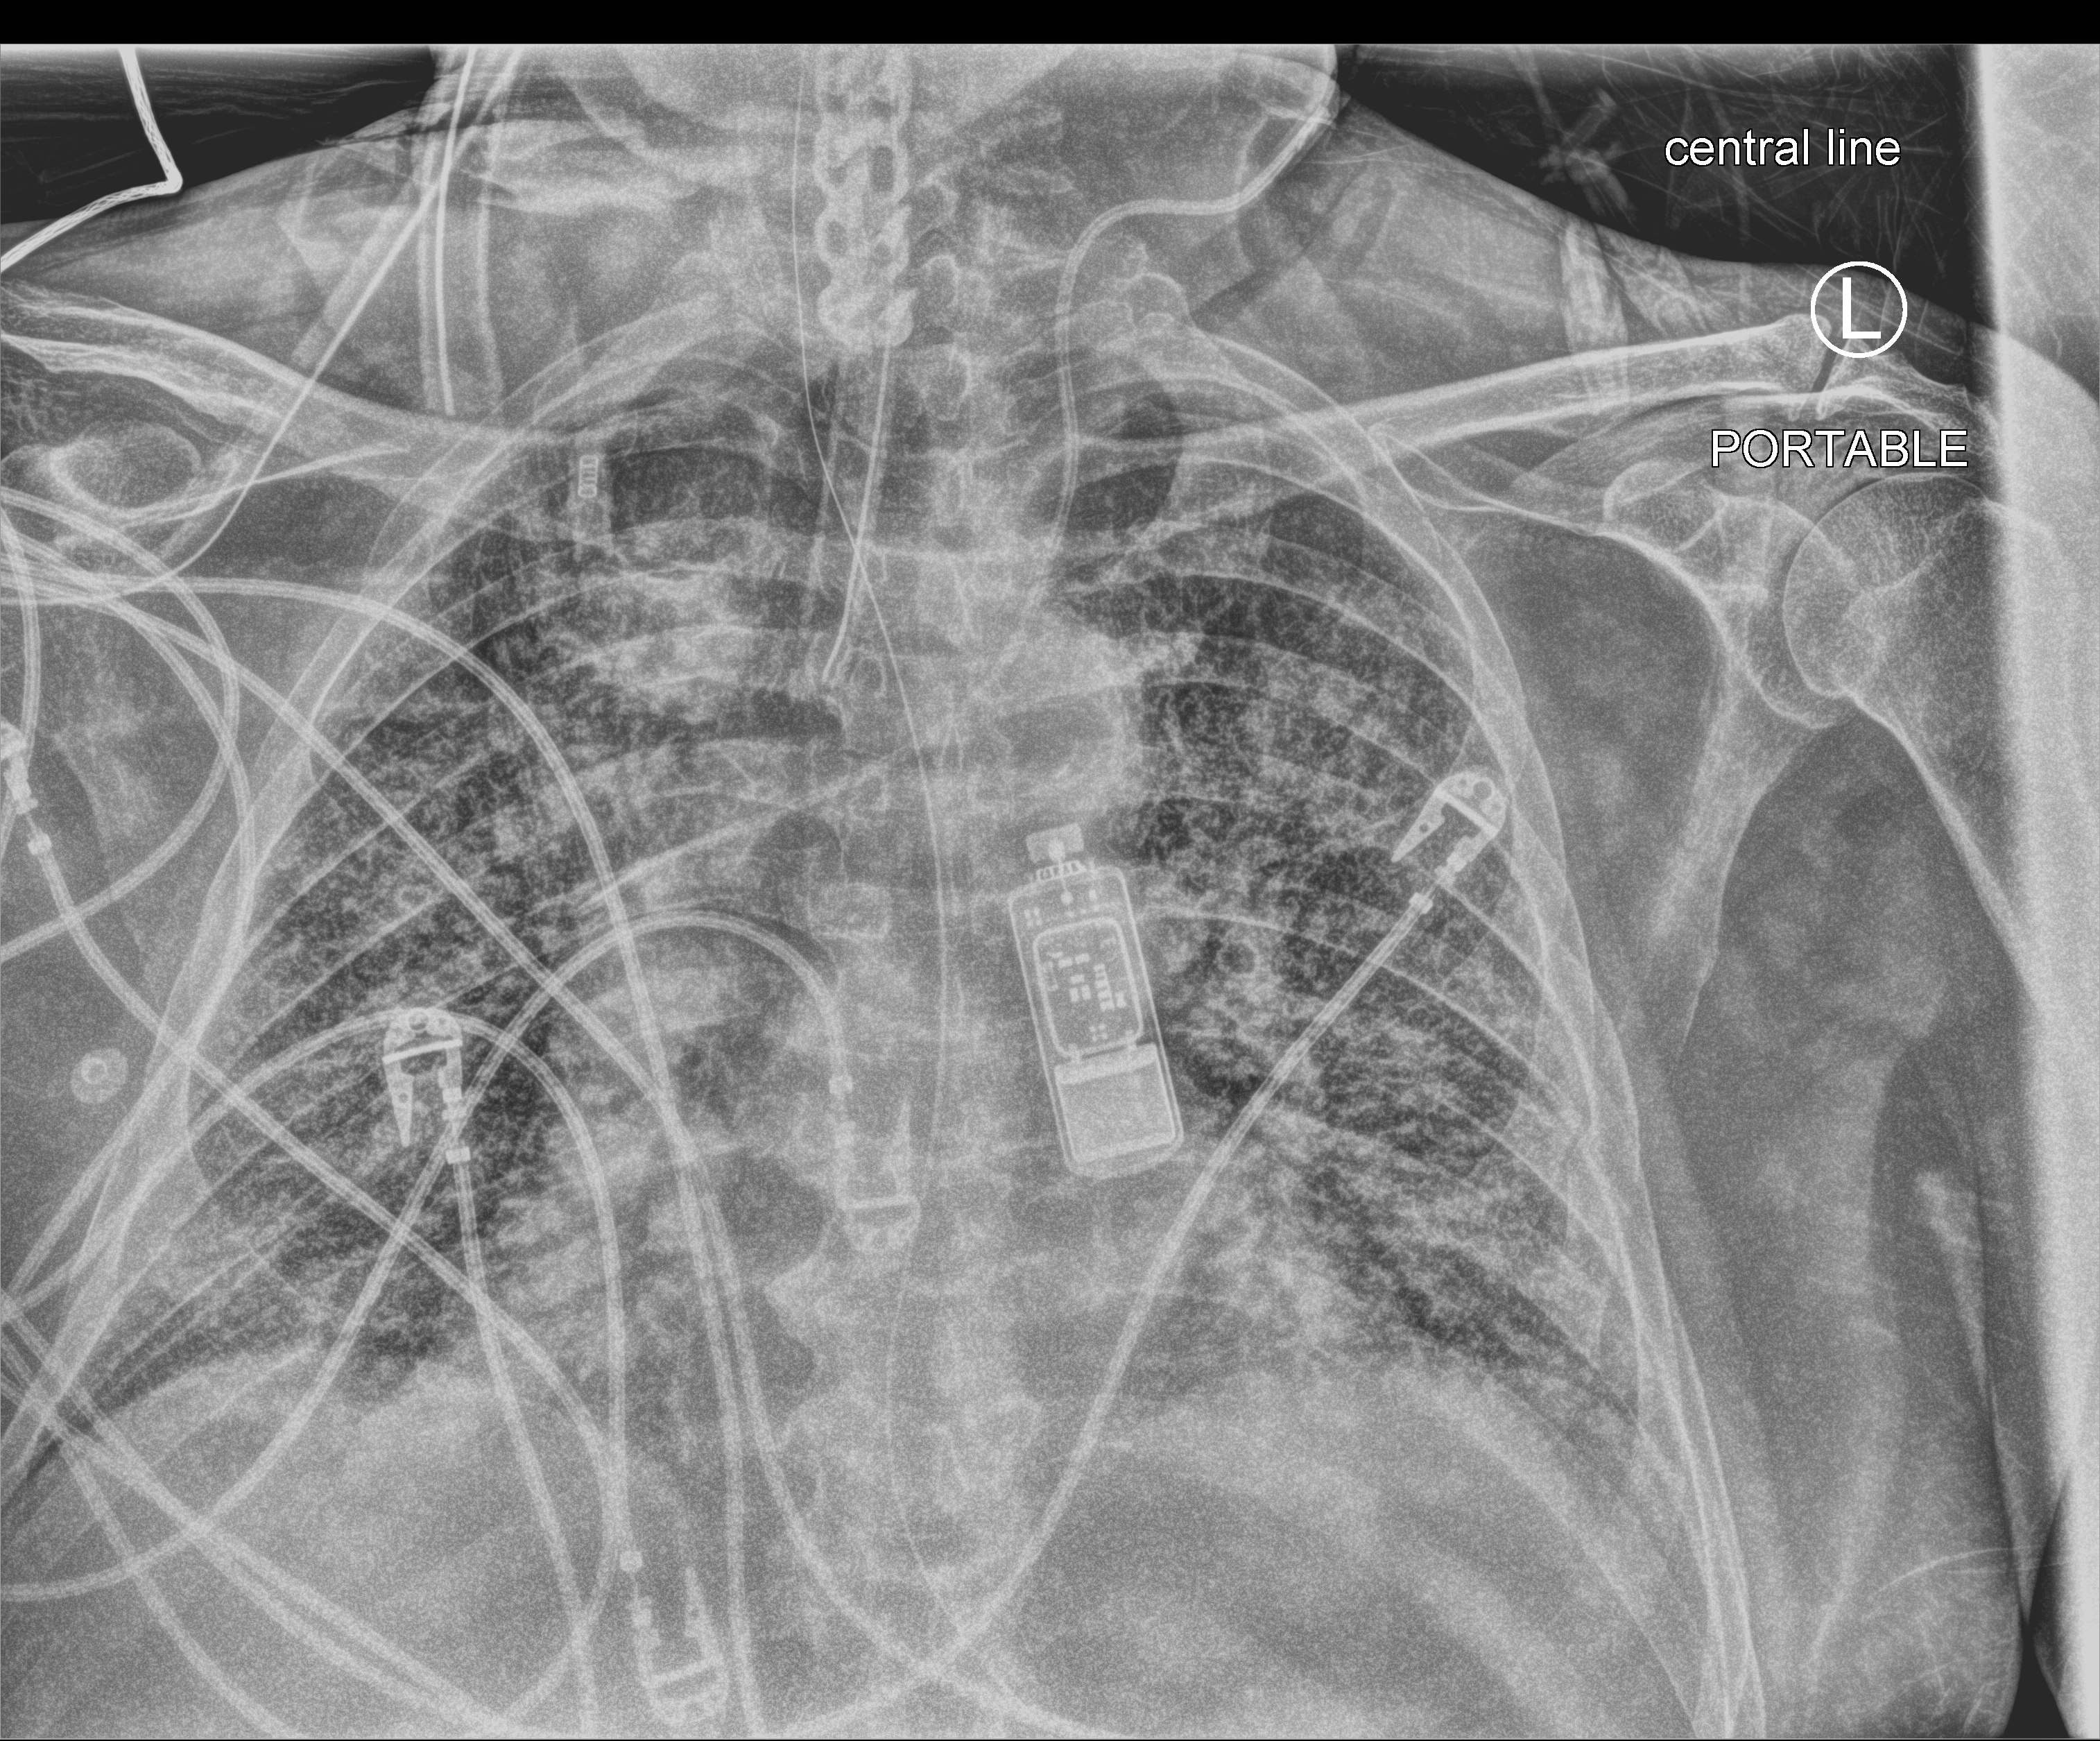
Chest X-ray (portable), anteroposterior (AP) projection. Male patient hospitalised with COVID-19, age 60–74 years.
From the hospital-stay record, not from the radiograph (when in the stay this image was taken is not recorded):
- length of hospital stay: 7 days
- smoking status (admission record): former
- COPD (admission record): no